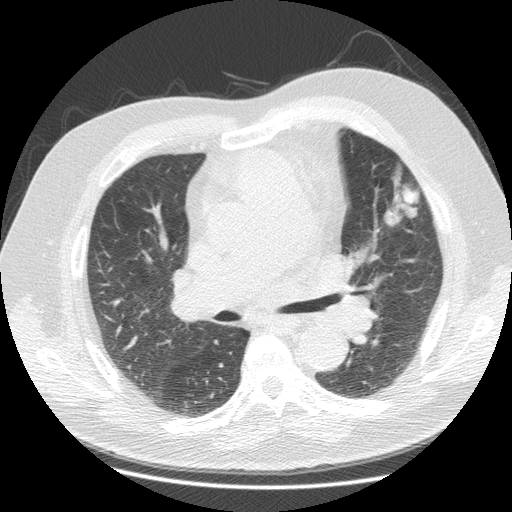
Low-dose screening chest CT, one axial slice. Slice 62 of 116 in the series (ordered by position). 140 kVp. Lung window (W 1500 / L -600 HU). 512 × 512 image matrix, field of view 390 × 390 mm.
Outlined on this slice (outlined manually by an expert reader):
- lesion 1 (tumor, upper lobe of left lung): bounding box <384,184,419,227> (left, top, right, bottom; pixels)